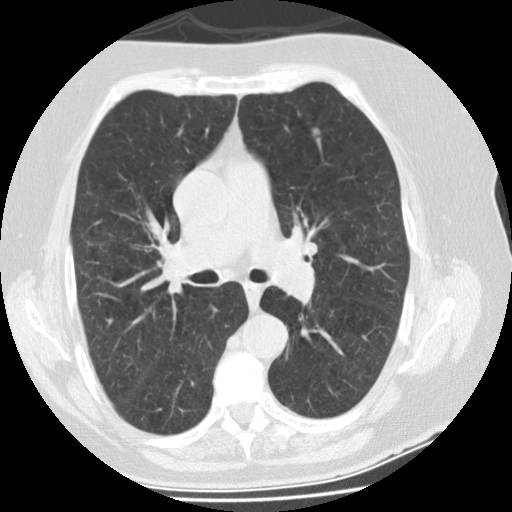
Axial slice from a low-dose chest CT screening exam; second annual screen; lung window (W 1500 / L -600 HU); 2.5 mm slice thickness. Female, age 74 years at enrolment.
- Lesion marked by an expert reader, bounding box <303,119,334,147> (left, top, right, bottom; pixels).
- The screening reader recorded 3 non-calcified nodules or masses ≥4 mm on this exam (right lower lobe, left upper lobe, left upper lobe); which of them this box marks is not recorded.
- Later outcome: lung cancer diagnosed 68 days after this screen — bronchiolo-alveolar adenocarcinoma, NOS, left upper lobe, stage IA (AJCC 6th edition), 20 mm at pathology.